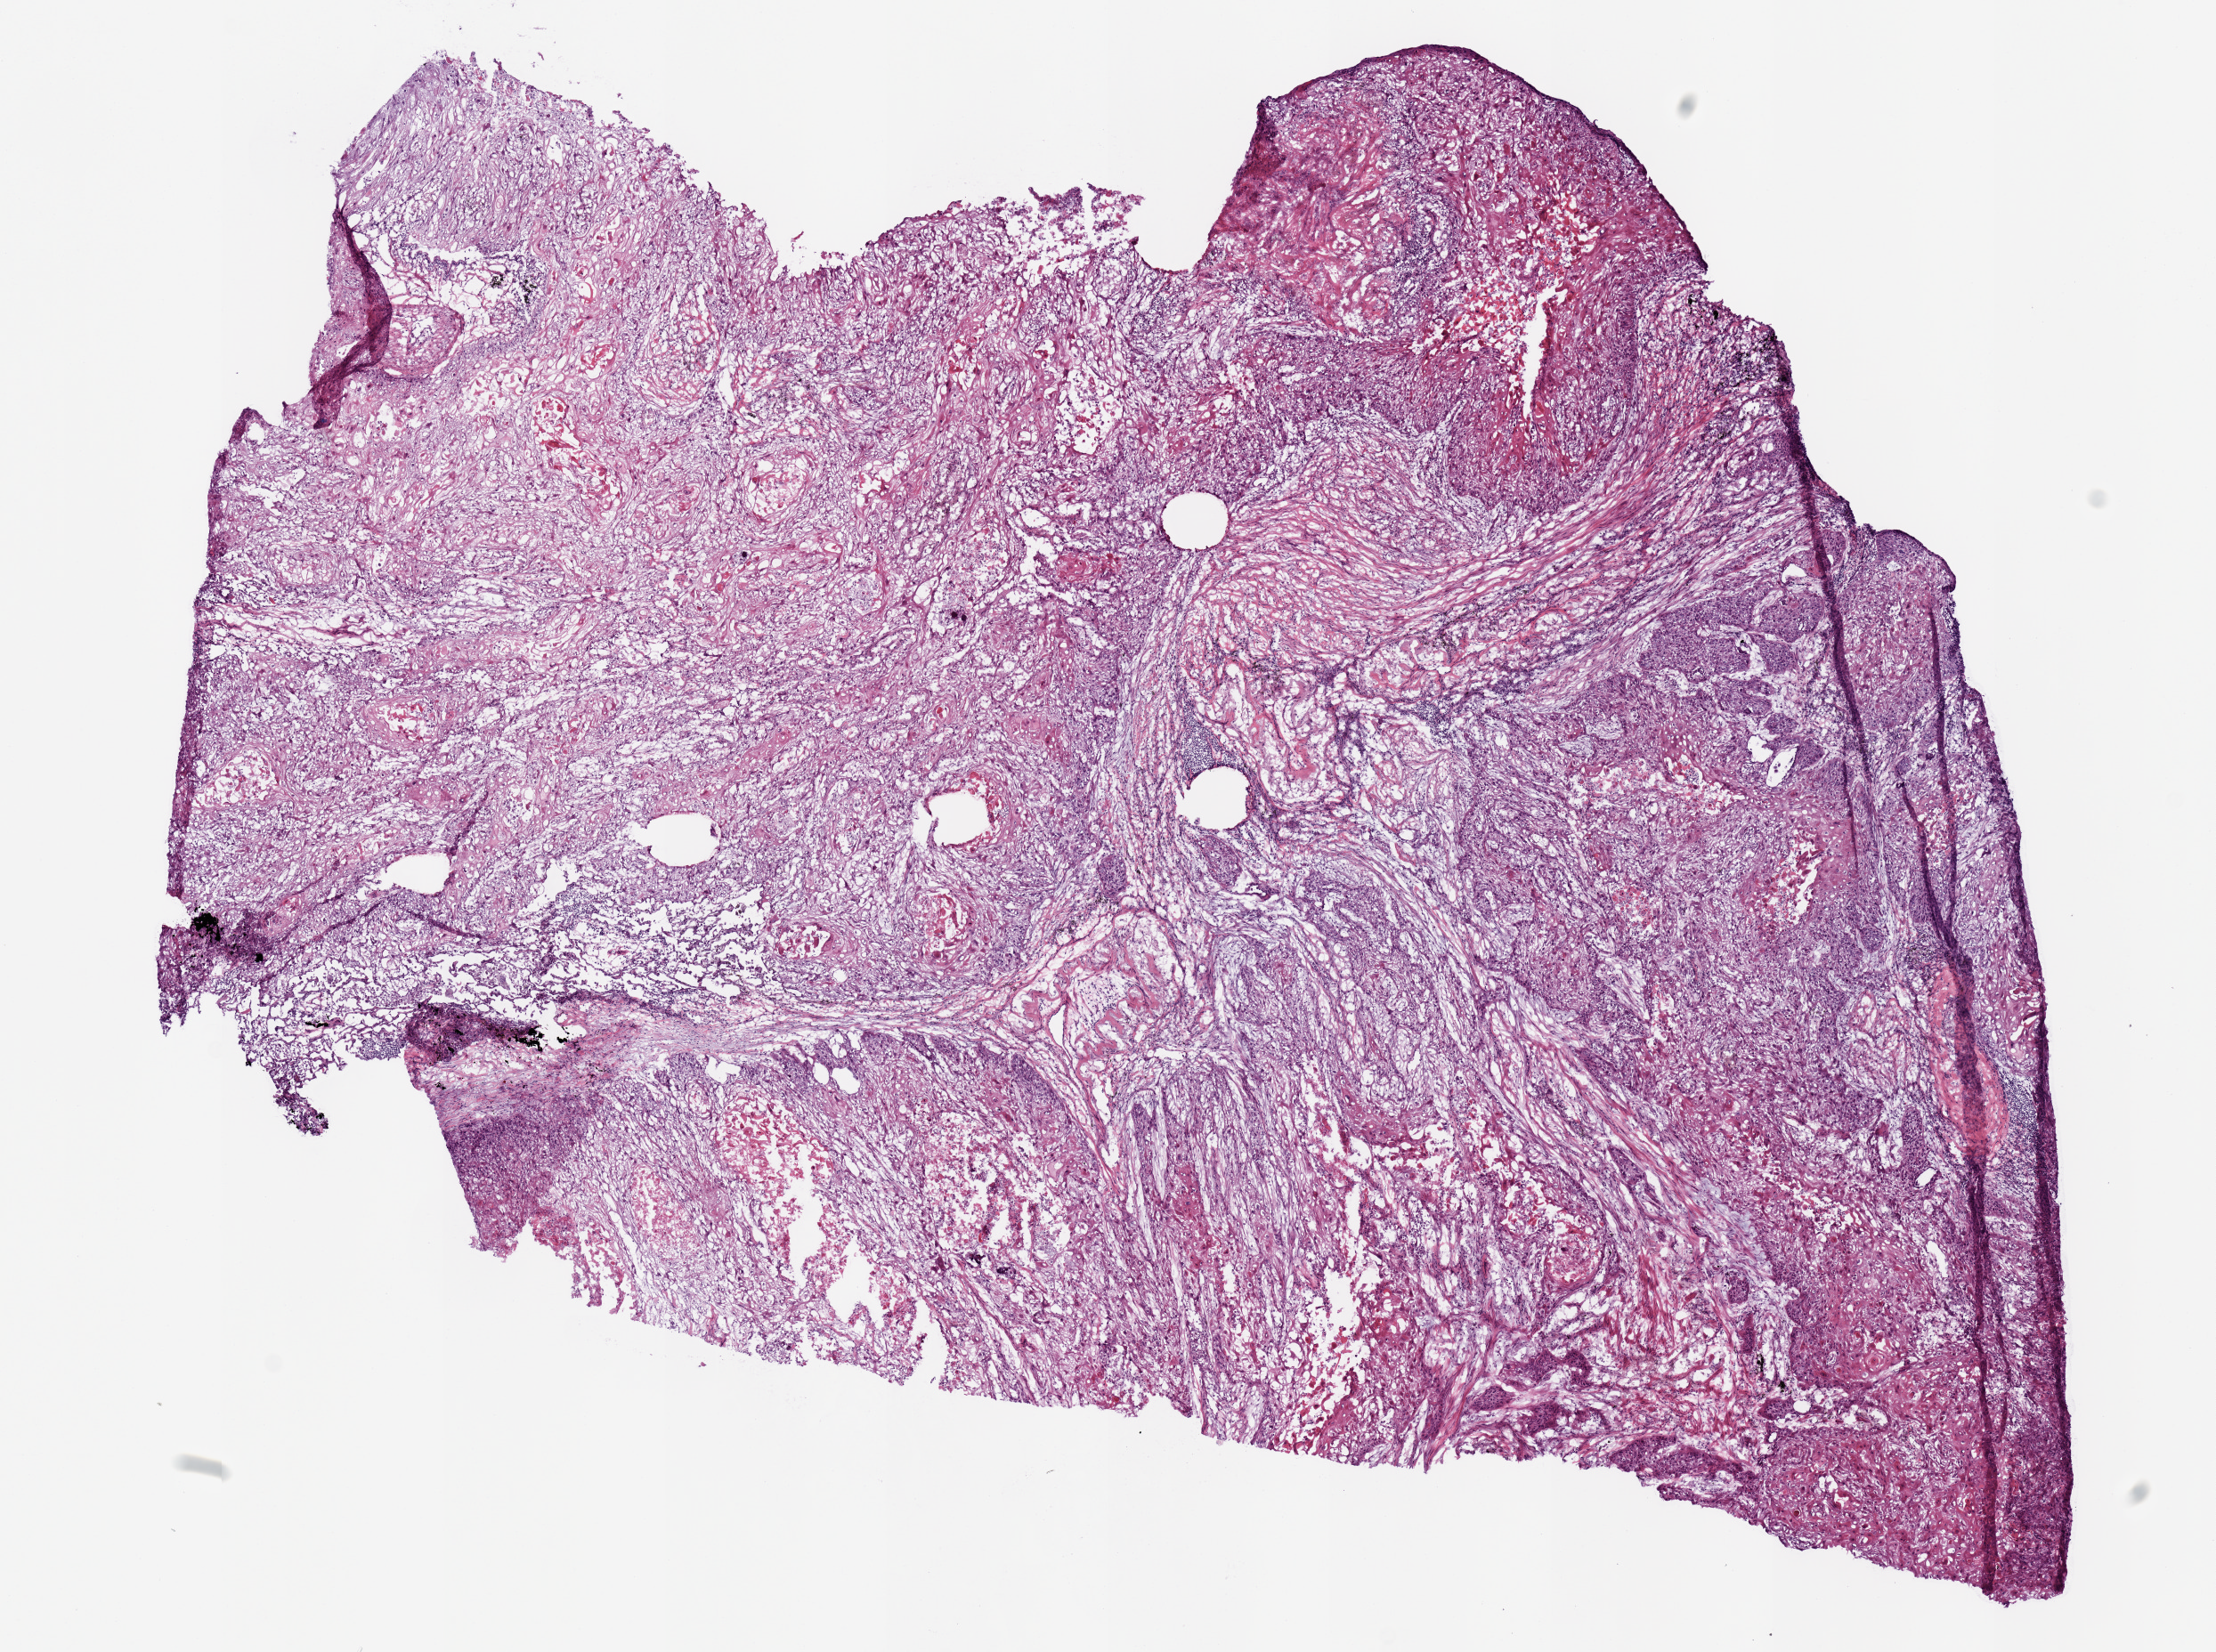
Hematoxylin and eosin (H&E) stained whole-slide image, shown as a low-resolution overview of the whole scanned area (about 9.8 x 7.3 mm). Frozen section. Lung, primary tumour sample. Male, age 75 years at initial diagnosis. Composition of this section per pathologist review: tumour cells 92%, tumour nuclei 80%, normal cells 0%, stromal cells 5%, necrosis 3%.
AJCC pathologic stage: IIB (7th edition). Histologic diagnosis: Squamous cell carcinoma, NOS.